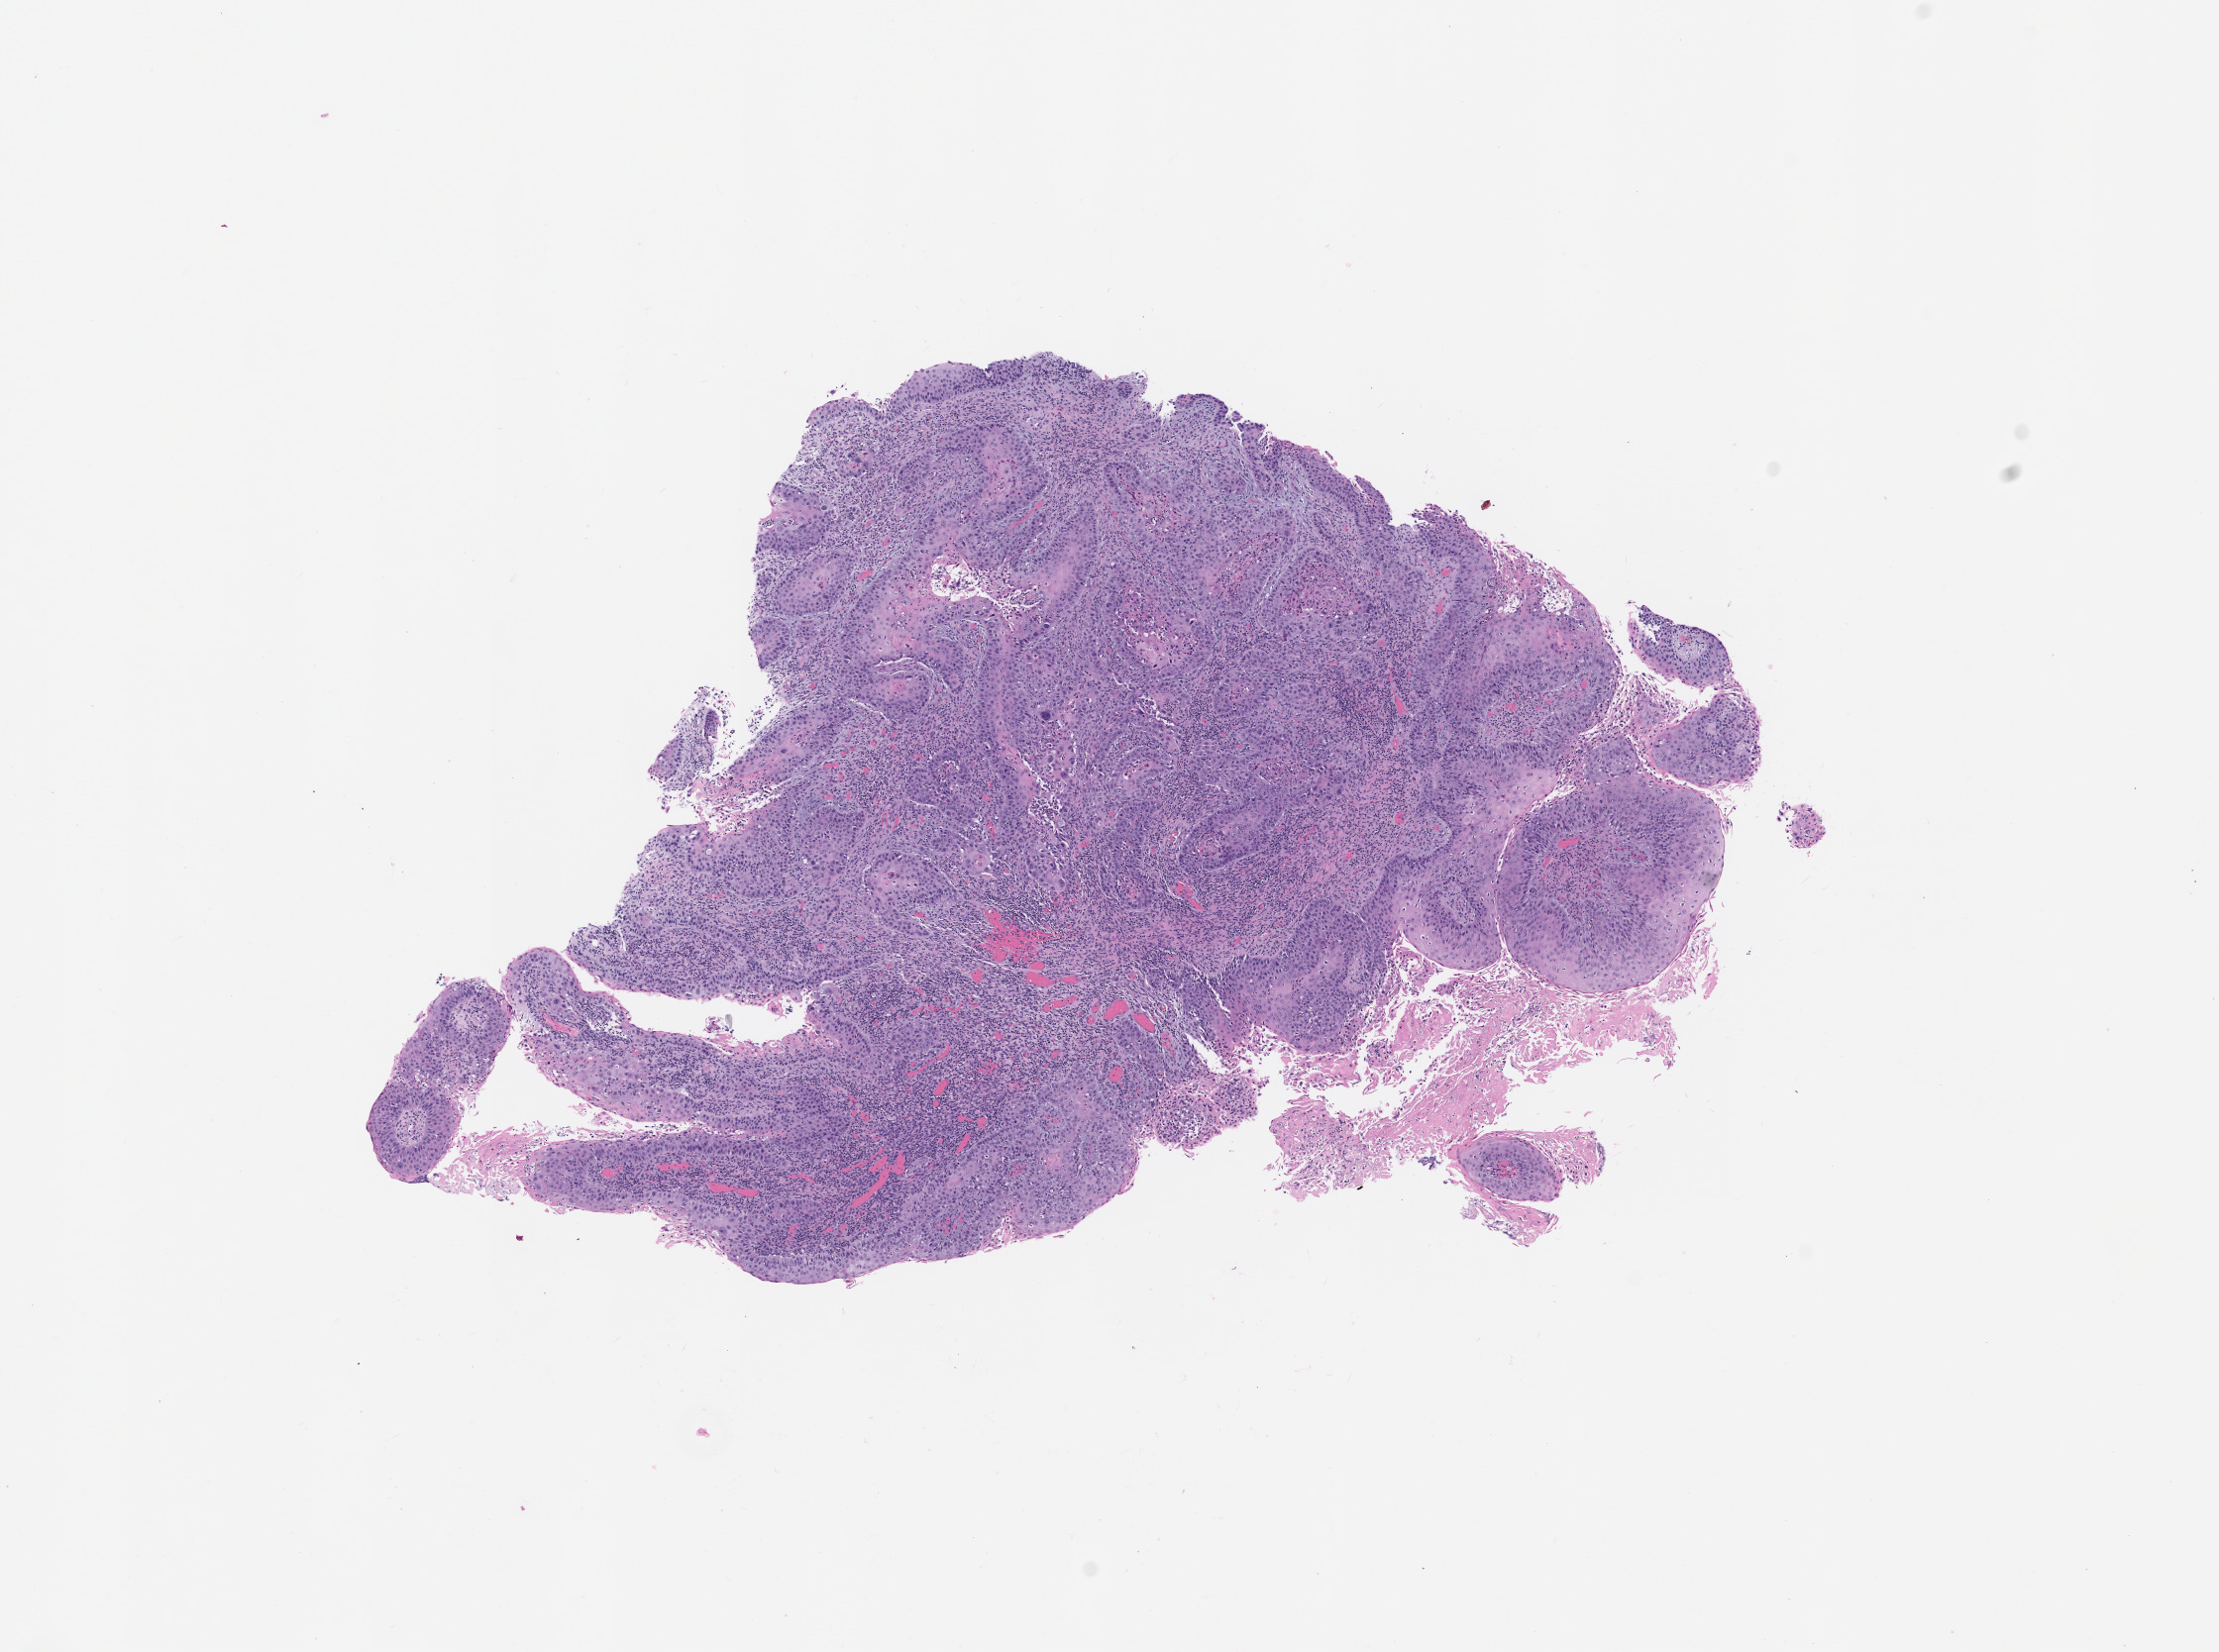
Digitized hematoxylin and eosin (H&E)-stained section of the patient's (originator) tumor tissue — a low-resolution overview of the entire scanned area, about 9.0 x 6.7 mm. FFPE section. Tumor site category: lung. Patient: female, 73 years old.
Diagnosis: Lung Squamous Cell Carcinoma.